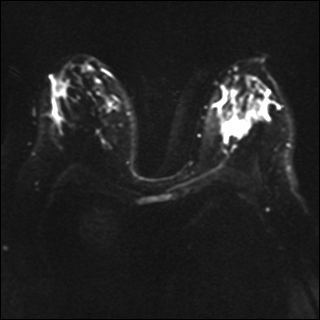
Breast MRI, one axial slice. Diffusion-weighted series; image 2 of 4 stored at this slice position (different b-values; order by instance number). 1.5 T. 4 mm slice thickness. 320 × 320 image matrix, field of view 340 × 340 mm. Female patient.
Structures marked on this image (outlined manually by an expert reader):
- tumour on diffusion-weighted imaging: box from (x=222, y=115) to (x=251, y=135) px